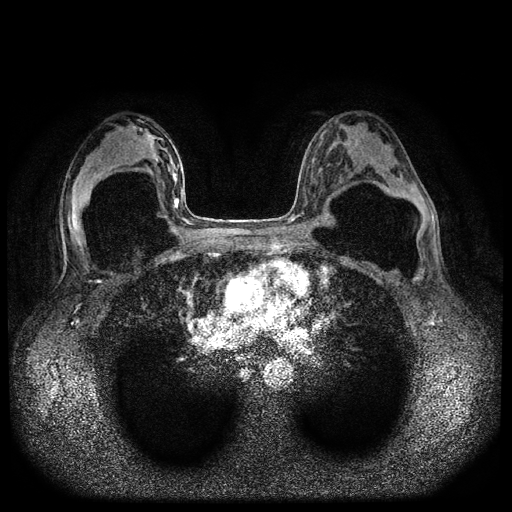
Breast MRI (dynamic contrast-enhanced, multi-phase), one axial slice; position 54 of 116 along the scan axis; dynamic contrast-enhanced series, time point 2 of 5 at this slice position (early post-contrast); 1.5 T; TE 2.6 ms, TR 5.4 ms; 2 mm slice thickness; 512 × 512 image matrix. Female patient, age 42 years.
Structures marked on this image (semi-automatic segmentation, software-assisted and operator-edited):
- breast lesion (labelled 'tumour' in the annotation; benign lesions carry a separate 'benign' label): bounding box <173,197,180,209> (left, top, right, bottom; pixels)